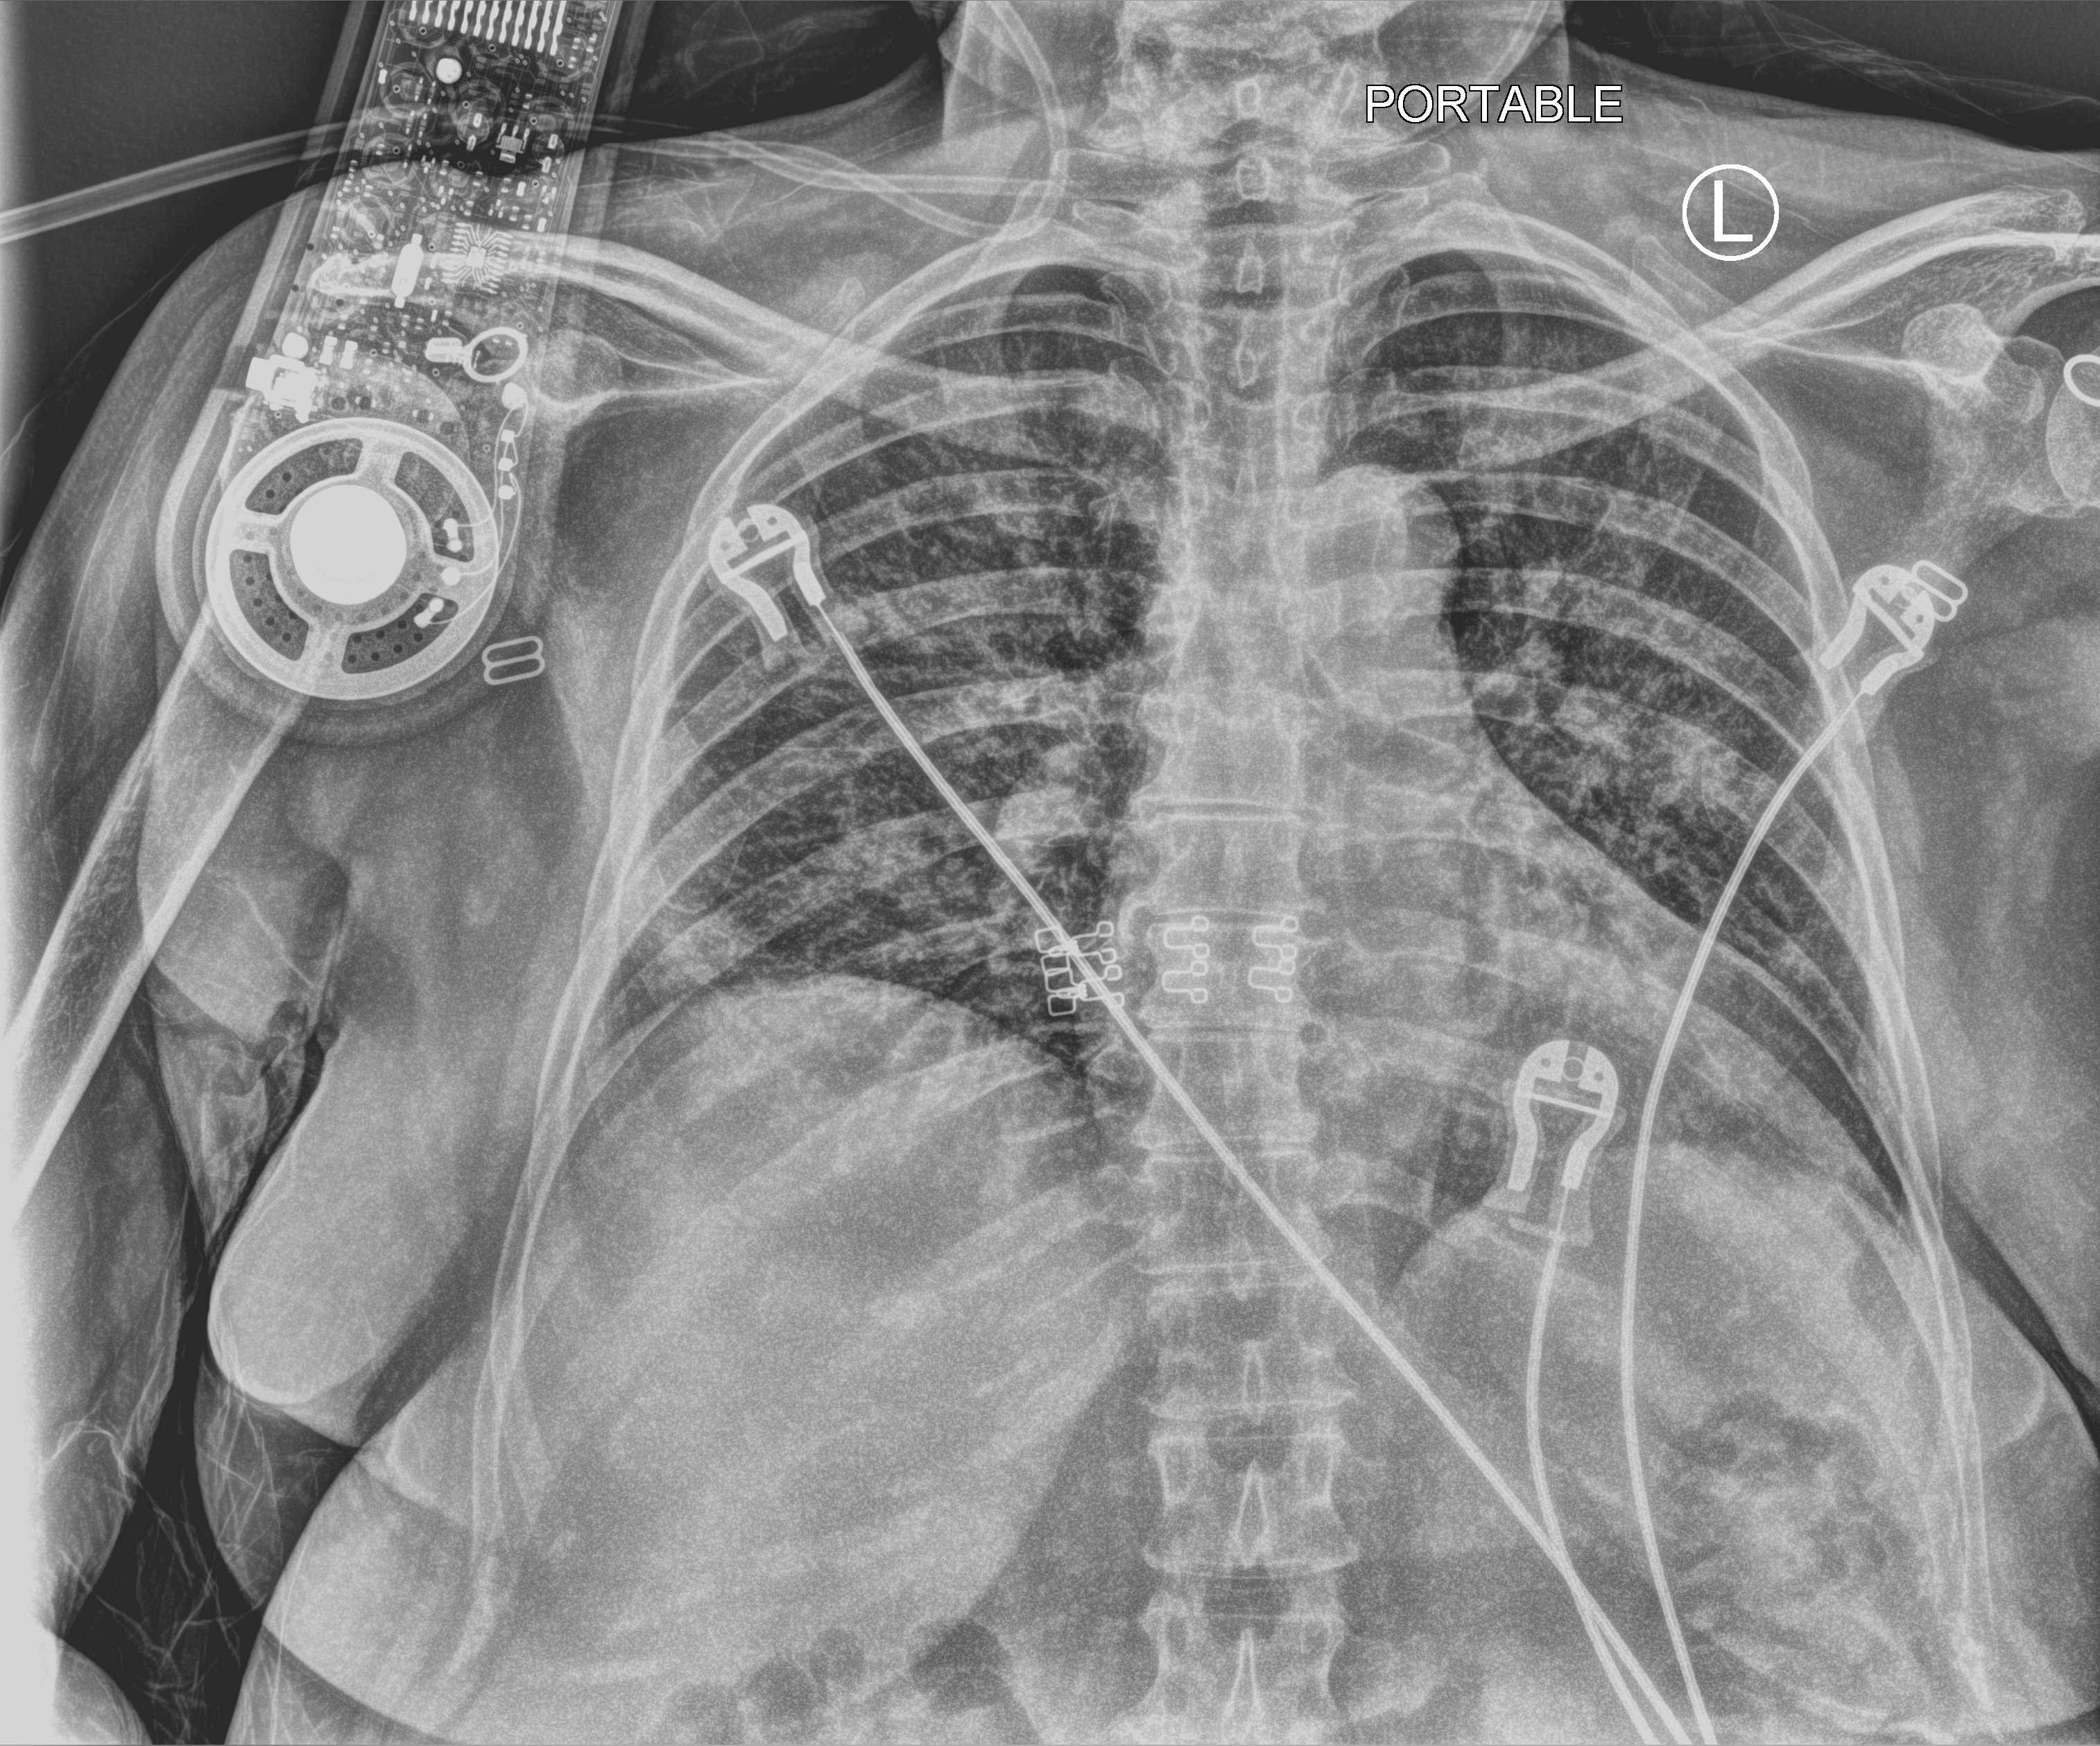
Bedside chest radiograph (computed radiography). Female patient hospitalised with COVID-19, age 60–74 years.
Admission-level facts for this patient (not findings on this image; timing relative to this image not recorded):
- mechanically ventilated during this hospital stay: no
- COPD (admission record): no